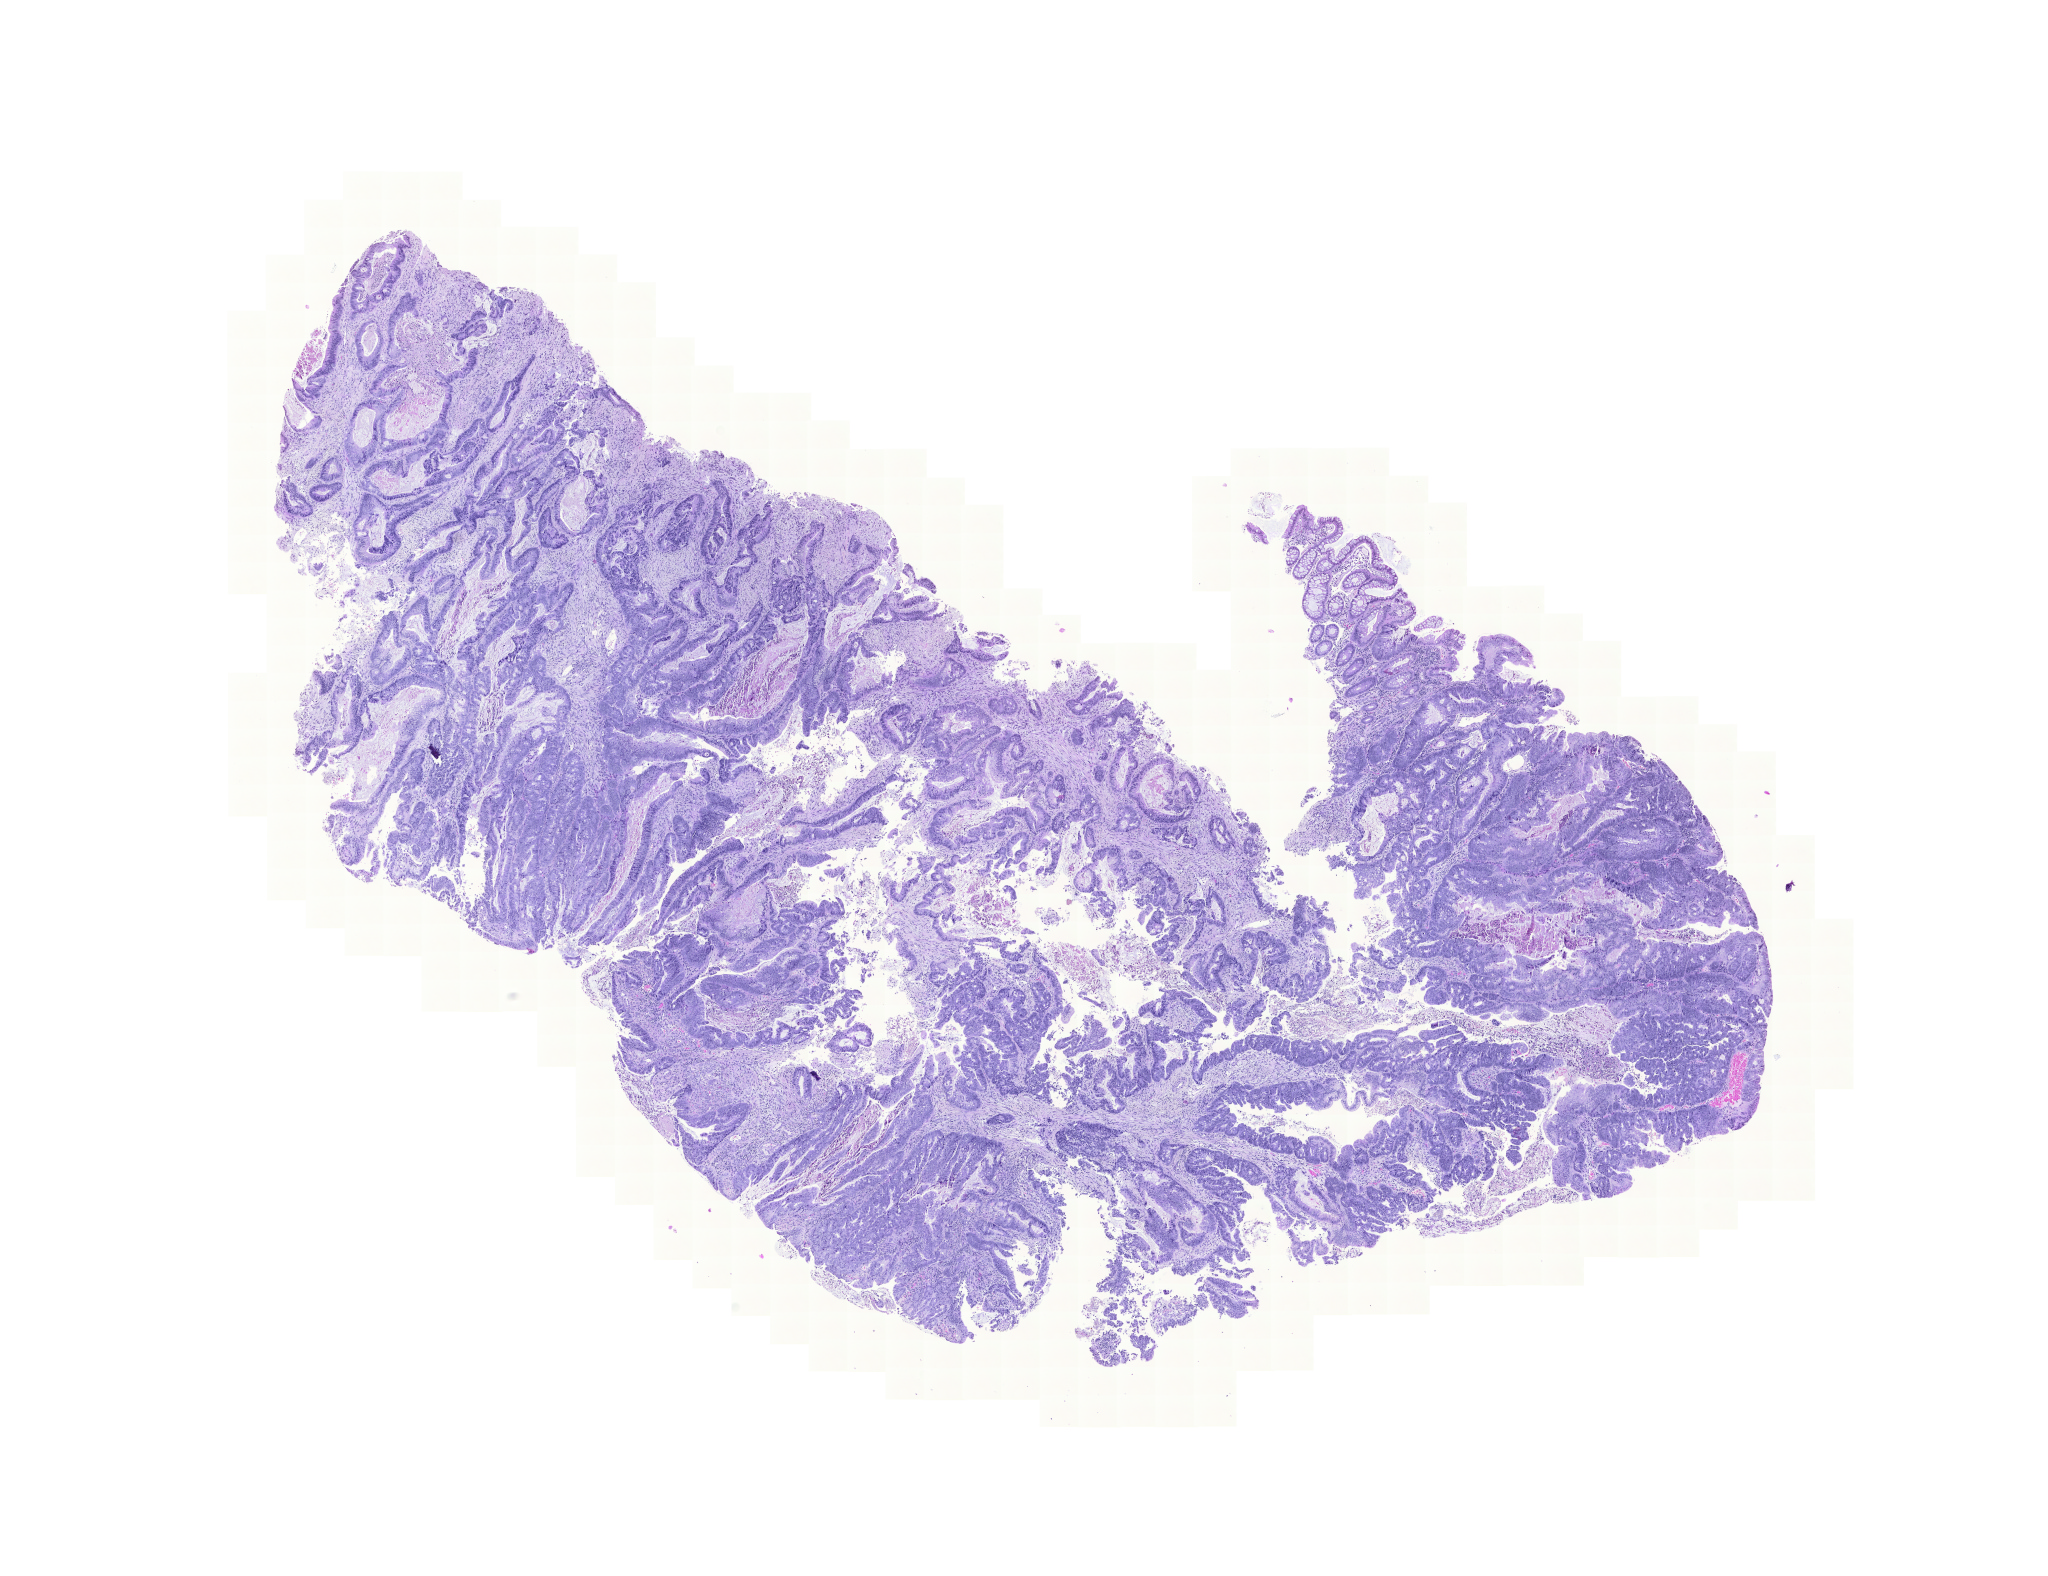
Digitized H&E tissue section (whole slide), shown as a low-resolution overview of the whole scanned area (about 15.2 x 11.7 mm), formalin-fixed paraffin-embedded (FFPE) diagnostic section, colon, primary tumour sample. Patient: male, age at initial diagnosis 79 years.
TNM: T3 N0 M0. AJCC pathologic stage: IIA. Histologic diagnosis: Adenocarcinoma, NOS (sigmoid colon).